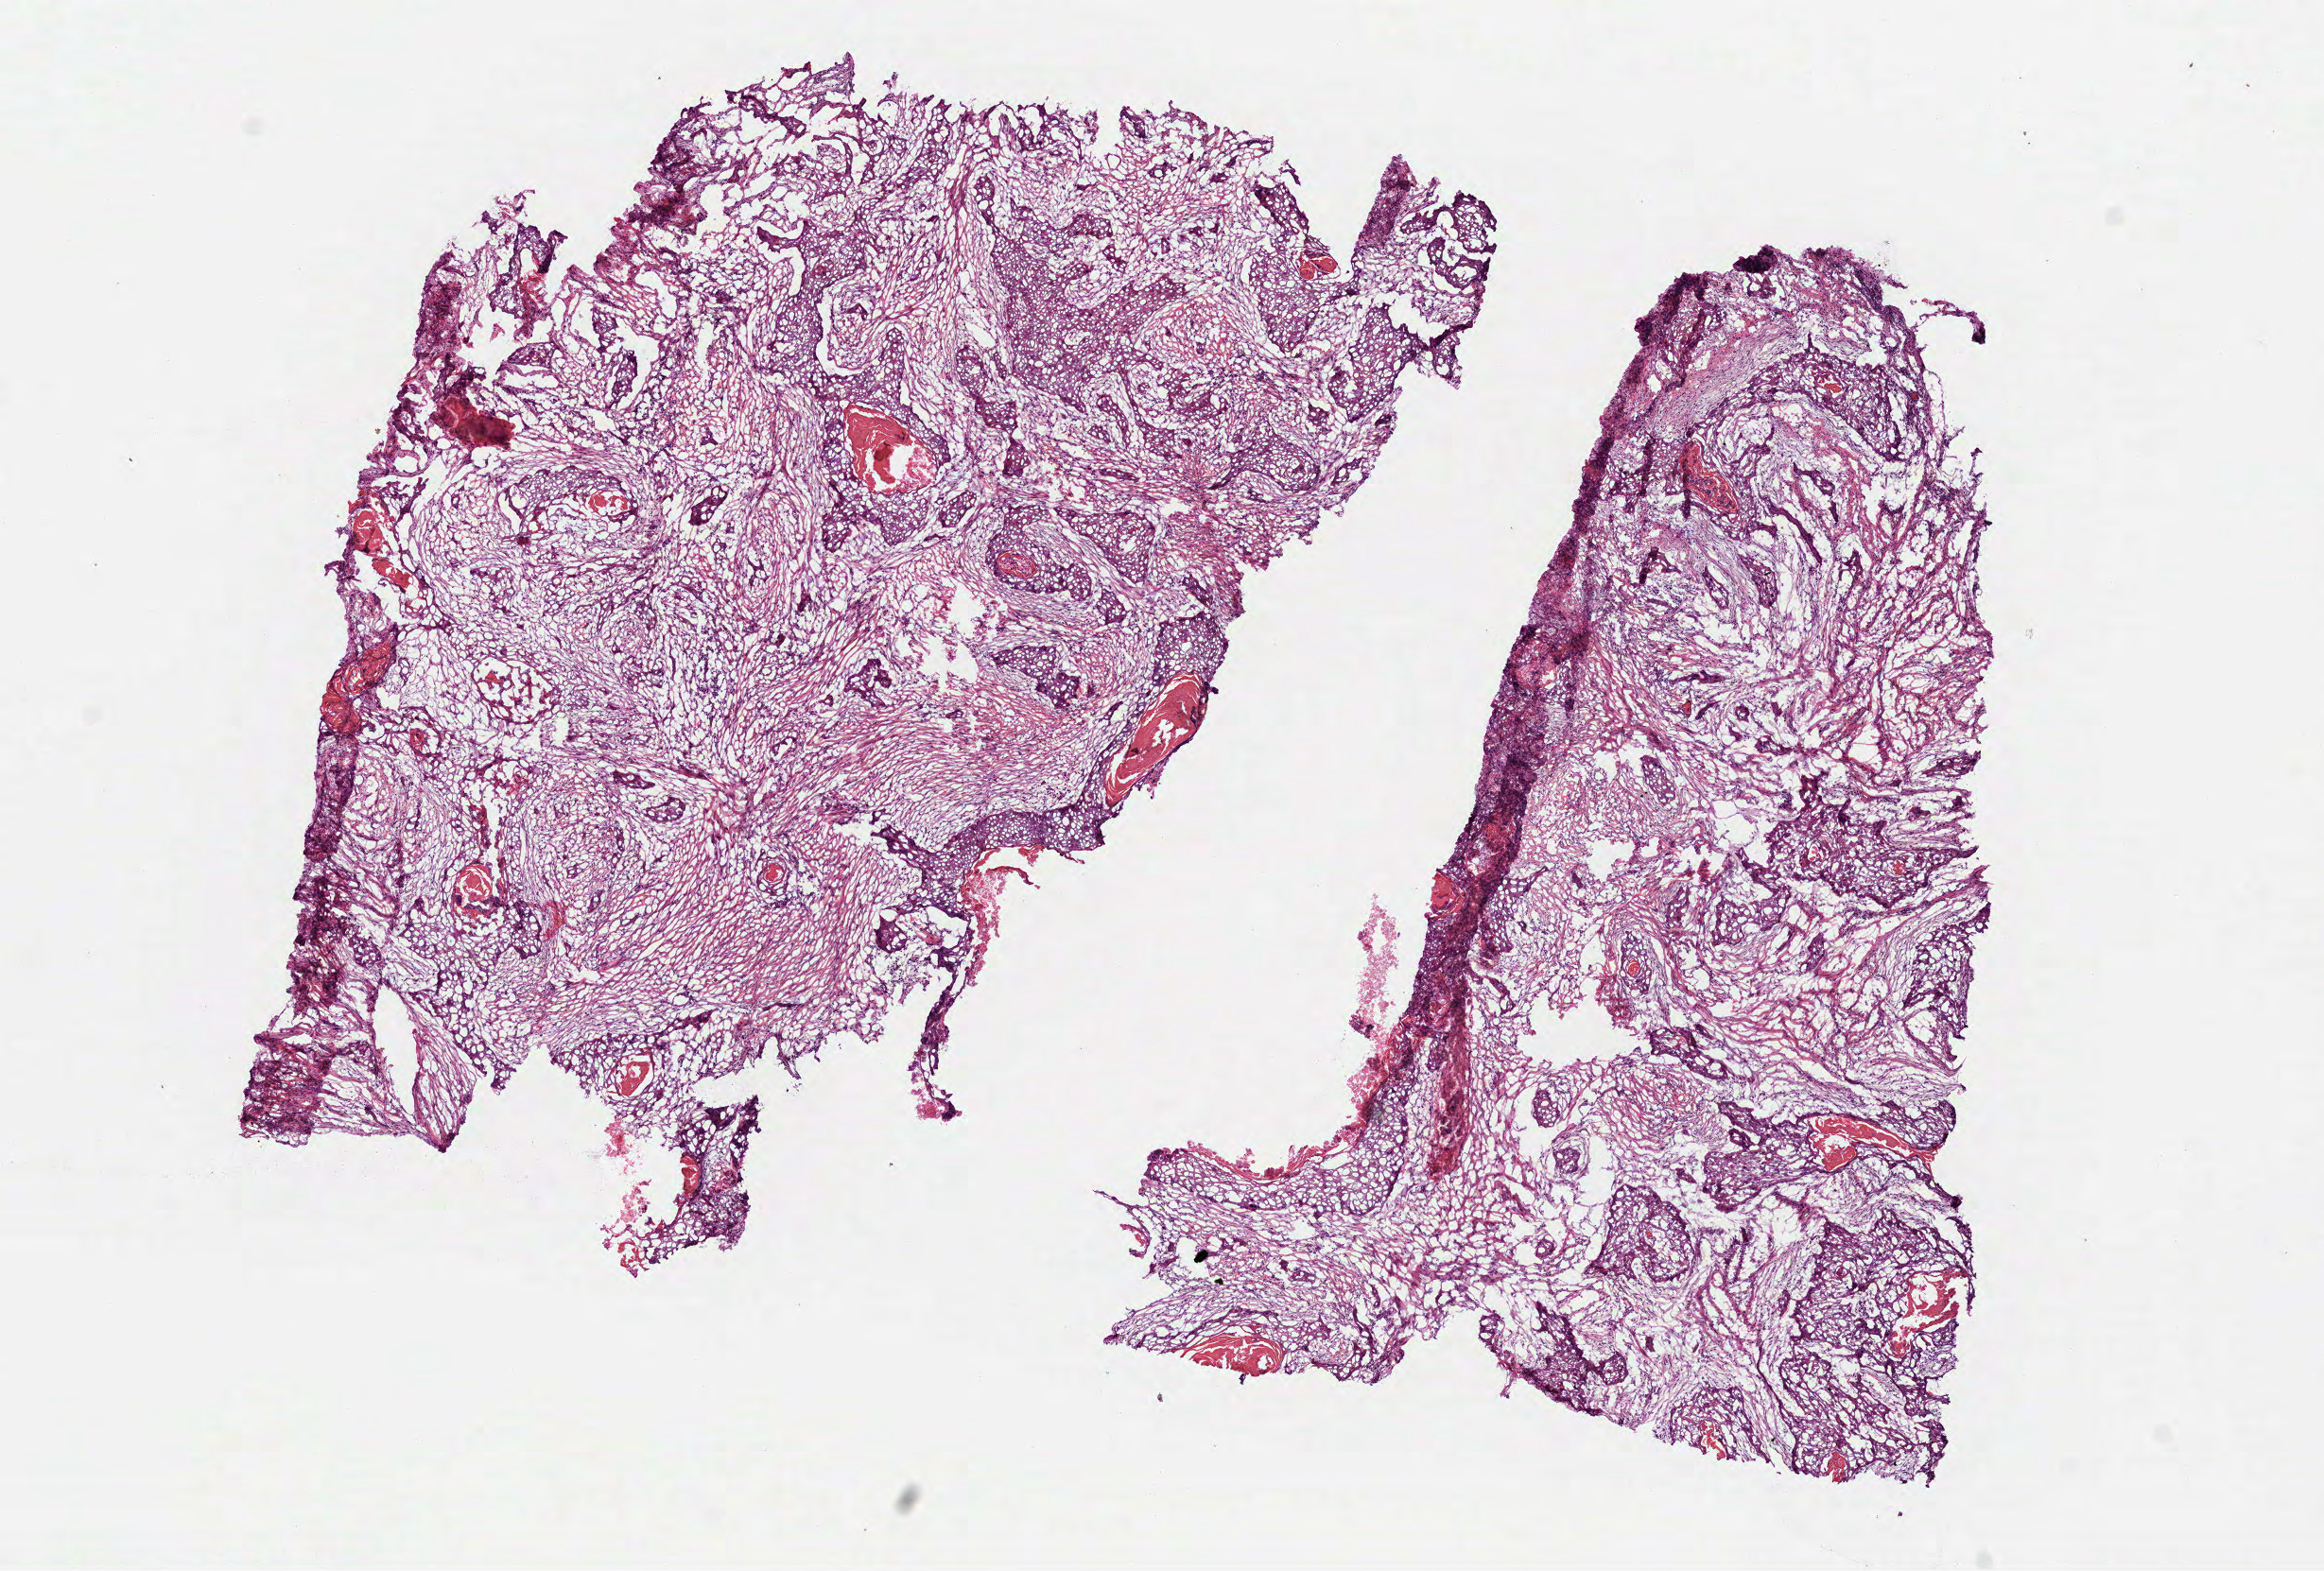
Digitized H&E tissue section (whole slide) — a low-resolution overview of the entire scanned area, about 9.9 x 6.7 mm (from a 40x scan). Frozen section from the bottom of the tissue portion. Sample: primary tumour, head and neck. Male patient; age at initial diagnosis 71 years. Composition of this section per pathologist review: tumour cells 93%, tumour nuclei 66%.
Diagnosis: Squamous cell carcinoma, NOS.